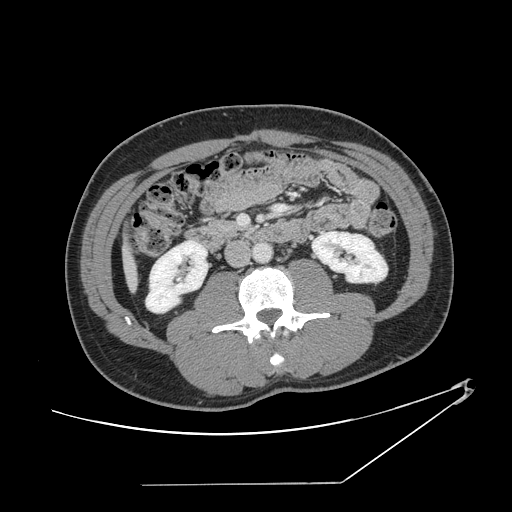
Contrast-enhanced abdominal CT, one axial slice. Position 41 of 152 along the scan axis. Reconstruction kernel STANDARD. Intravenous contrast given. Soft-tissue window (W 400 / L 40 HU). 2.5 mm slice thickness. 512 × 512 image matrix, field of view 432 × 432 mm. Male patient, age 45 years. Case-level facts recorded for this patient, not image findings: diagnosis: colorectal cancer liver metastases, imaged before liver resection; multiple liver metastases: no; largest metastasis: 1 cm; disease in both lobes: no.
Structures marked on this image (manually delineated by an expert):
- liver: box from (x=125, y=253) to (x=136, y=286) px
- planned liver remnant (the part of the liver to remain after resection): (x=125, y=253)–(x=136, y=287)